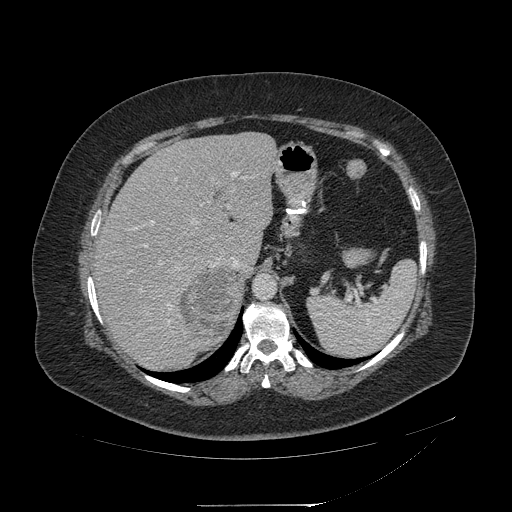
Contrast-enhanced abdominal CT, one axial slice. Reconstruction kernel STANDARD. 120 kVp. Intravenous contrast given. Soft-tissue window (W 400 / L 40 HU). 1.25 mm slice thickness. 512 × 512 image matrix, field of view 453 × 453 mm. Female patient, age 55 years. Case-level facts recorded for this patient, not image findings: diagnosis: adrenocortical carcinoma; tumour side: right adrenal; tumour size at pathology: 11 cm; Ki-67 index: 20 %; stage (as recorded): 2.
Annotated regions visible in this slice (semi-automatic segmentation, software-assisted and operator-edited):
- mass: bounding box <181,268,238,338> (left, top, right, bottom; pixels)